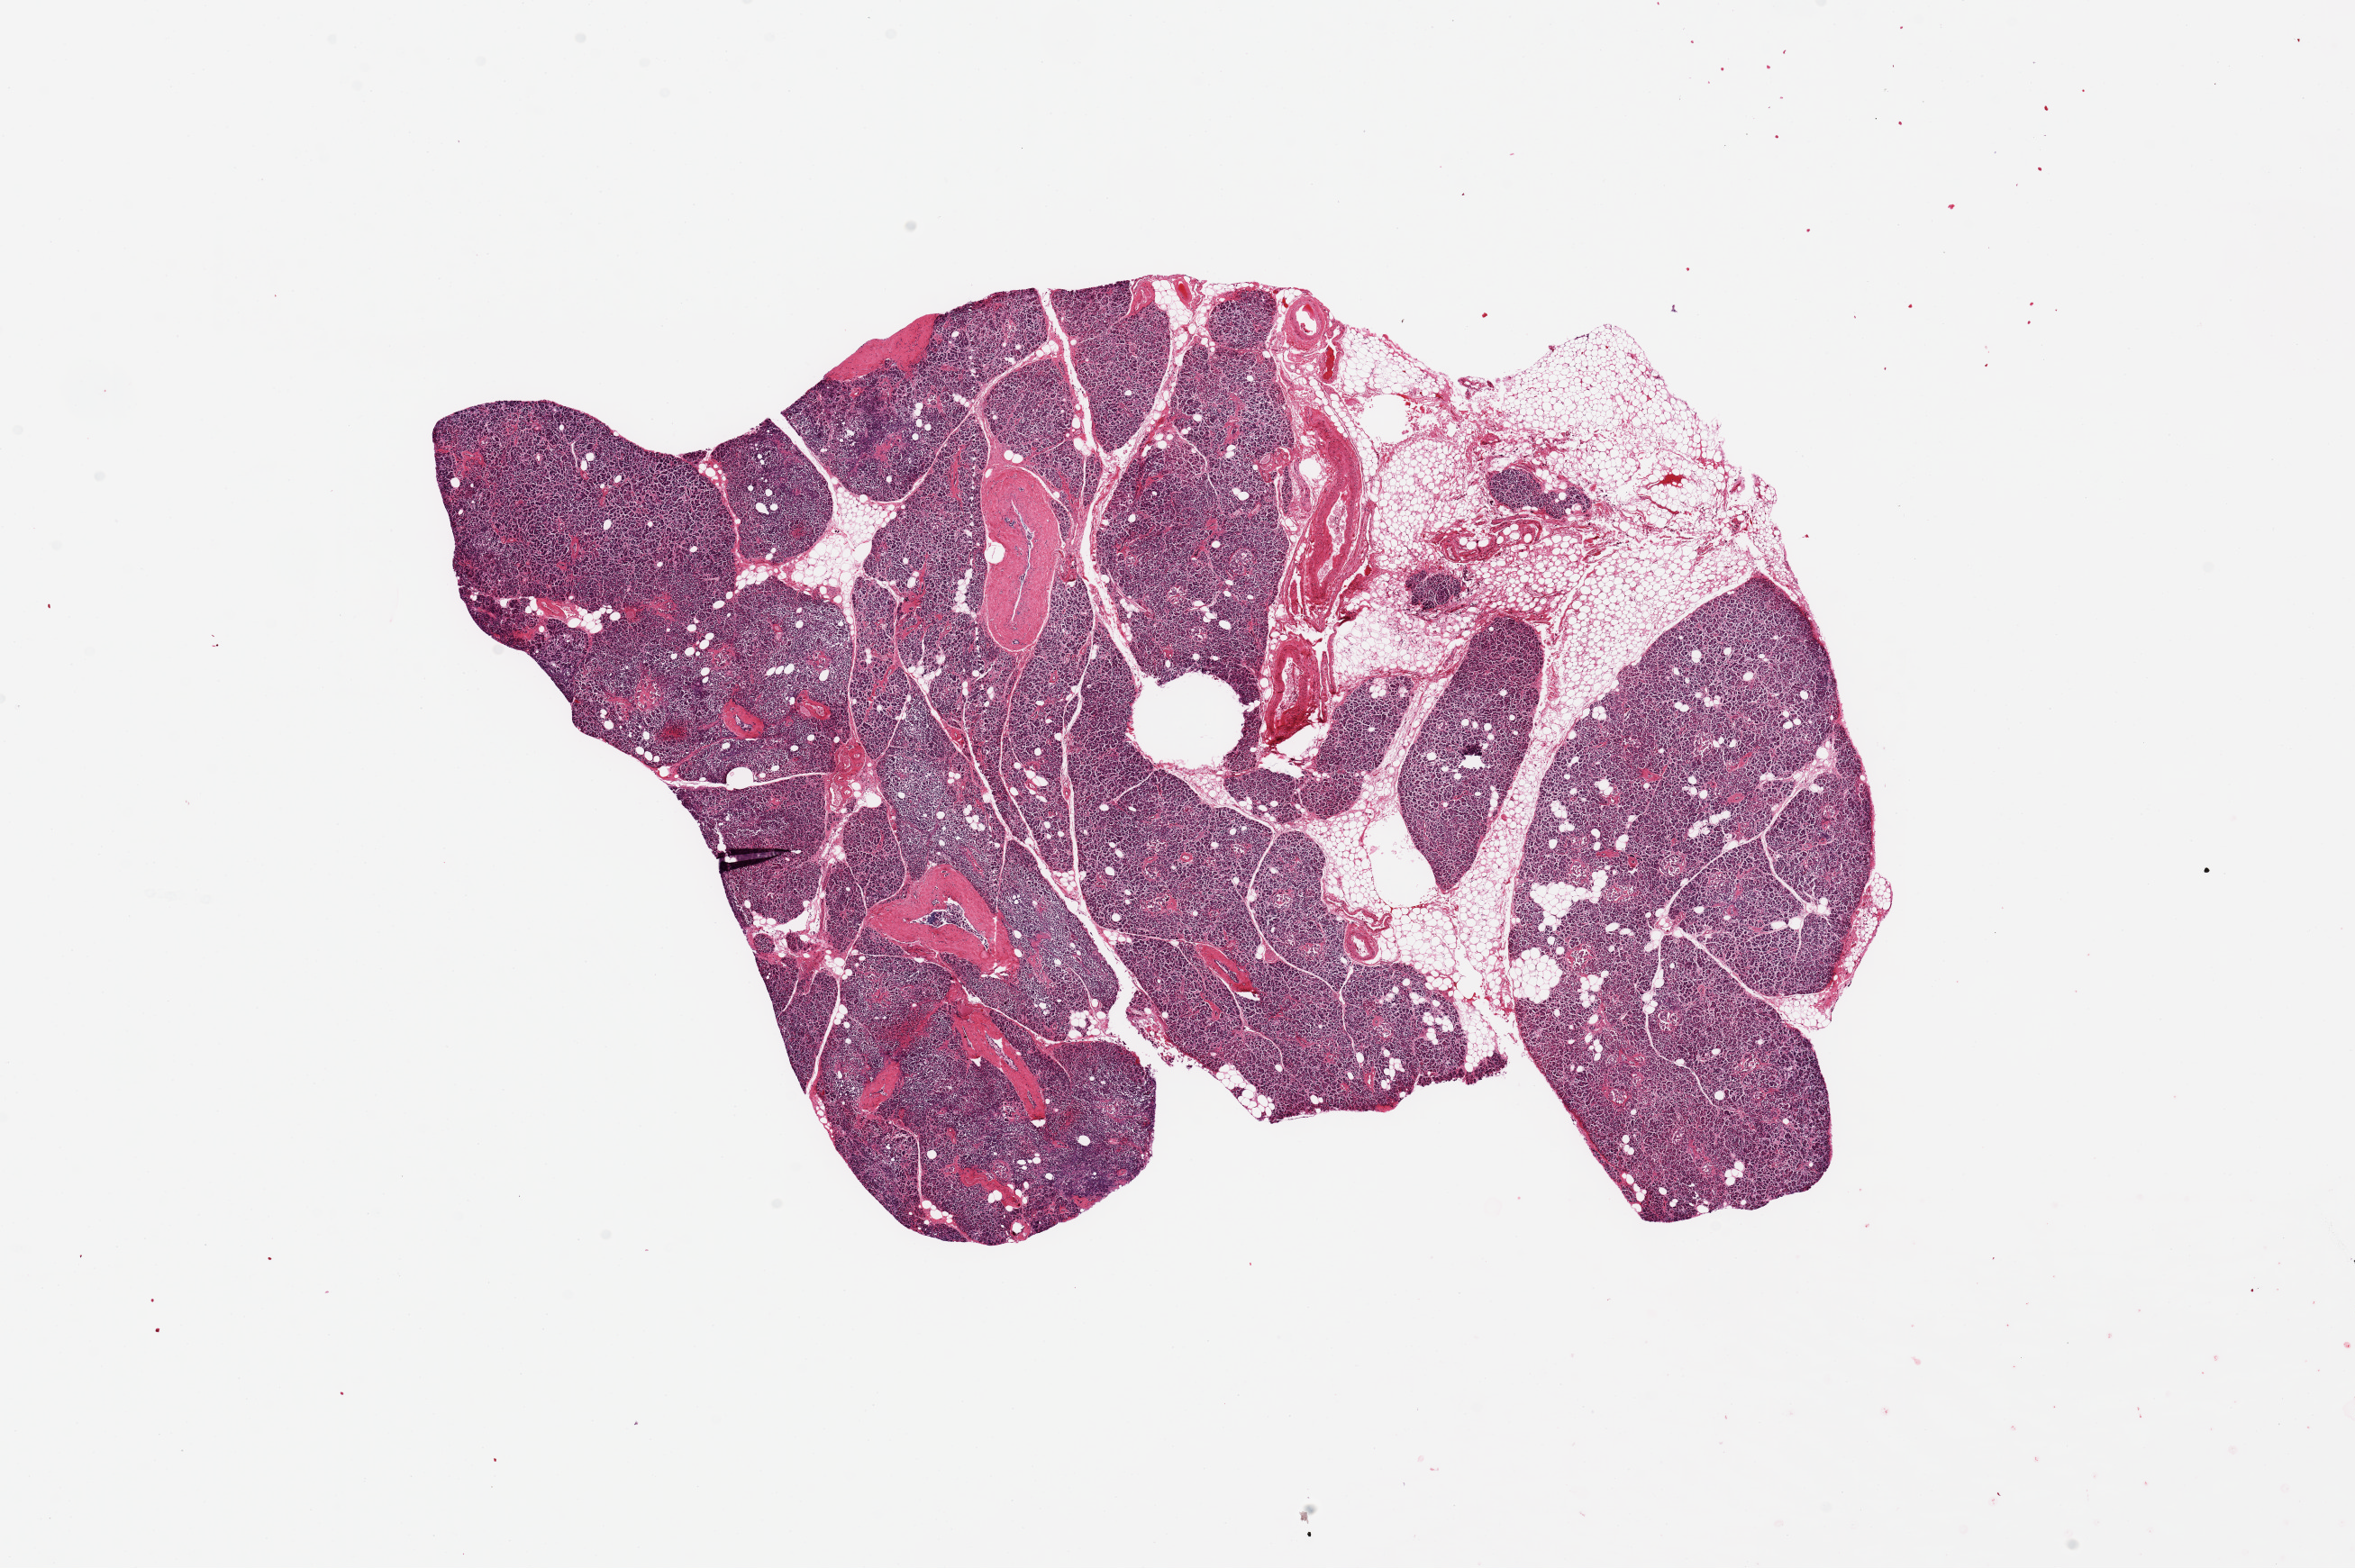
Whole-slide image, H&E stain, brightfield — shown as a low-resolution overview of the whole scanned area (about 20.7 x 13.8 mm, from a 20x scan), PAXgene-fixed, paraffin-embedded tissue, target tissue: pancreas, donor tissue sample. Female donor.
Review note (as recorded): 10x8 mm; good parenchymal preservation; autolysis of ducts; ~10% of aliquot is adipose.